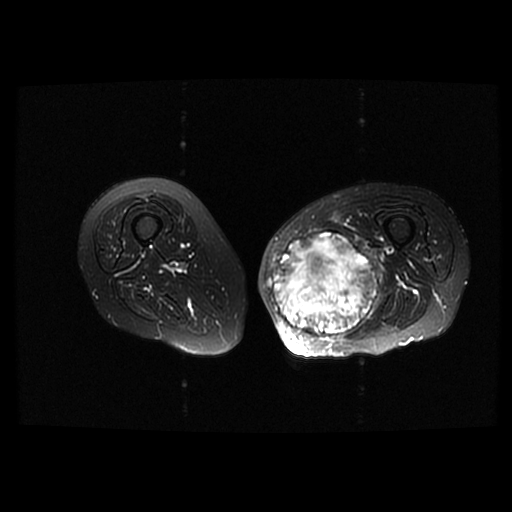
MRI of an extremity soft-tissue mass, one axial slice; position 31 of 42 along the scan axis; T2-weighted fat-saturated; 6 mm slice thickness; 512 × 512 image matrix. Female patient. Case-level facts recorded for this patient, not image findings: histological type: pleomorphic leiomyosarcoma; grade: high; site of the primary tumour: left thigh.
Outlined on this slice (expert manual segmentation):
- gross tumour volume including surrounding oedema: box from (x=263, y=230) to (x=384, y=338) px
- gross tumour volume (mass): (x=263, y=231)–(x=378, y=338)